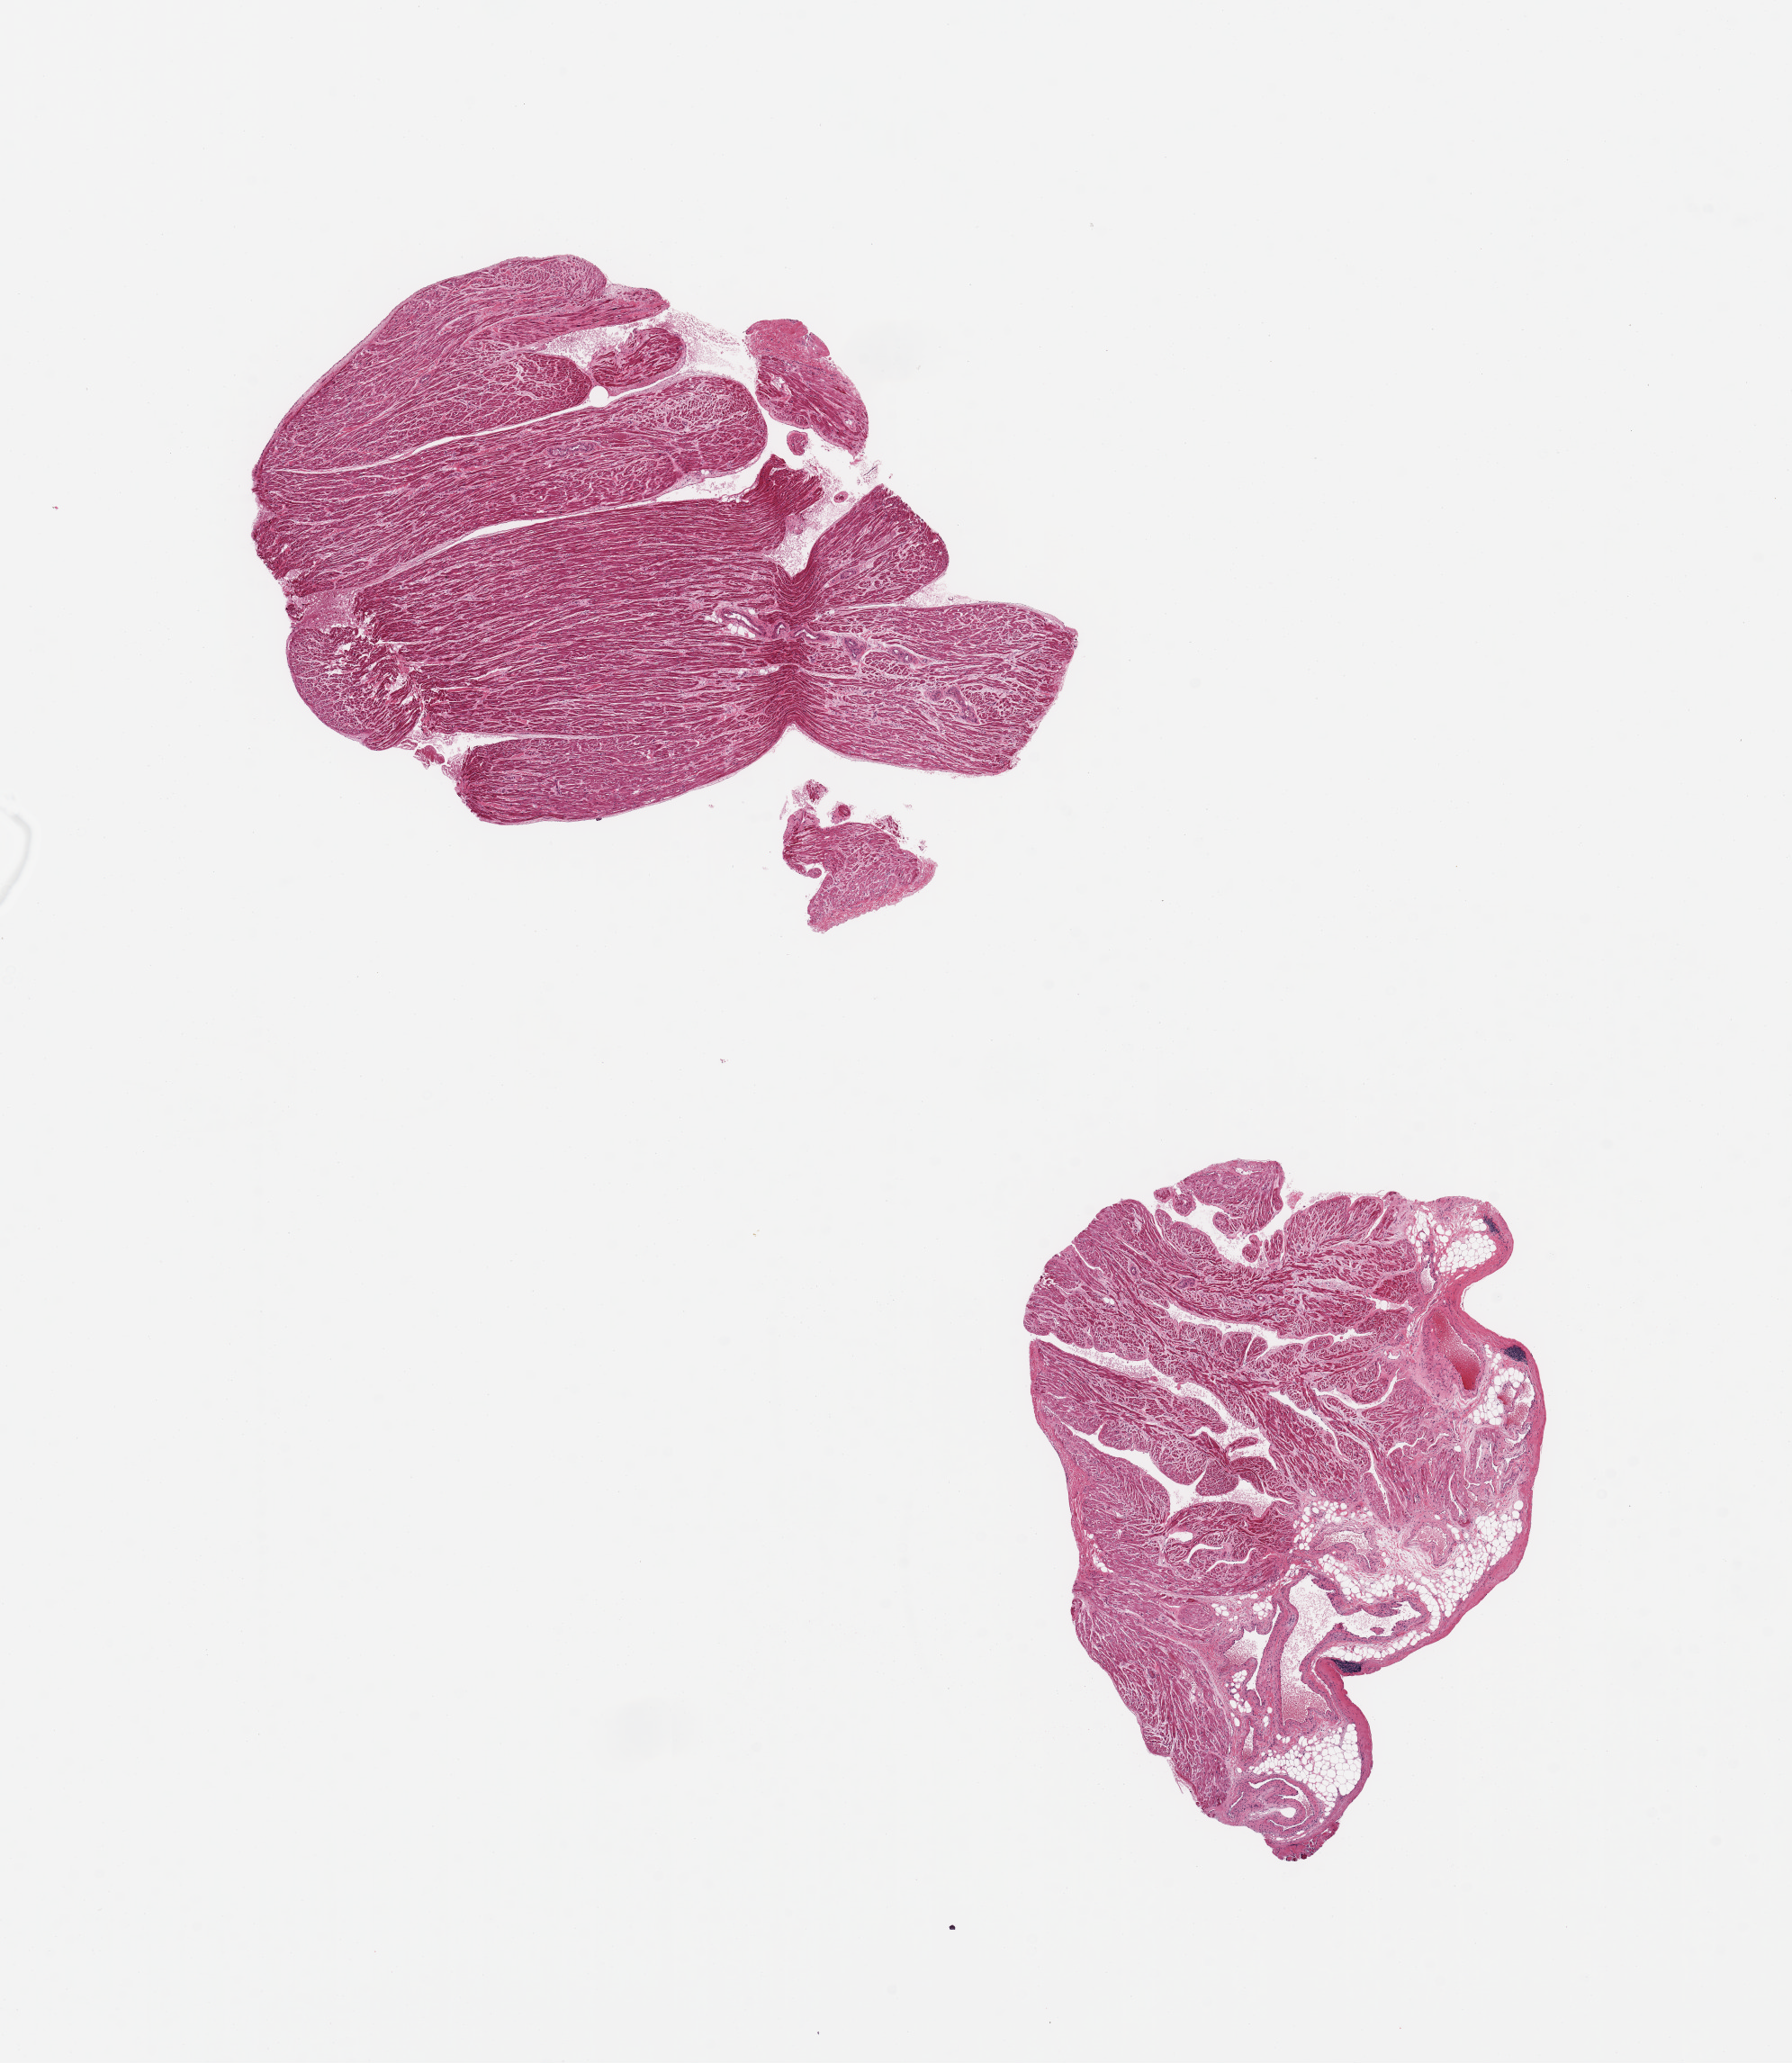
Digitized haematoxylin and eosin-stained section, brightfield — whole scanned area (about 15.8 x 18.1 mm) shown as a low-resolution overview; PAXgene-fixed paraffin-embedded (PFPE) section; section of auricular appendage (target tissue); tissue donor sample. Donor sex: male.
- pathologist's review note for this sample: 2 pieces; small lymphoid aggregates